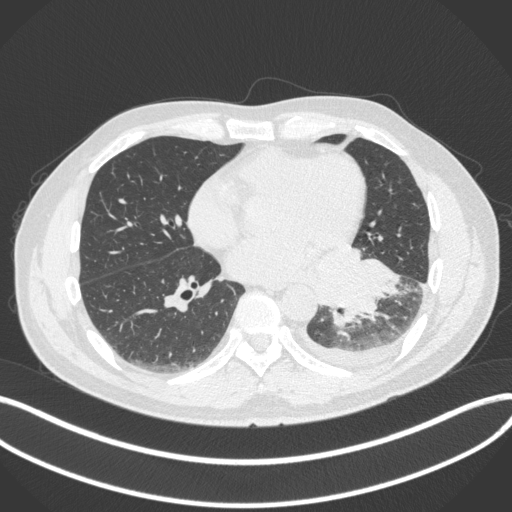
Chest CT, one axial slice. Slice 150 of 350 in the series (ordered by position). Reconstruction kernel B31f. 120 kVp. Lung window (W 1500 / L -600 HU). 1 mm slice thickness. 512 × 512 image matrix, field of view 400 × 400 mm. Patient: male, 58 years. From the clinical record (not read from this slice): clinical TNM (as recorded): T3 N1 M1b; histopathological grade: G3.
Structures marked on this image (bounding box drawn by a radiologist):
- lung tumour (recorded histology: small cell carcinoma): bounding box [x1, y1, x2, y2] px = [331, 250, 402, 329]